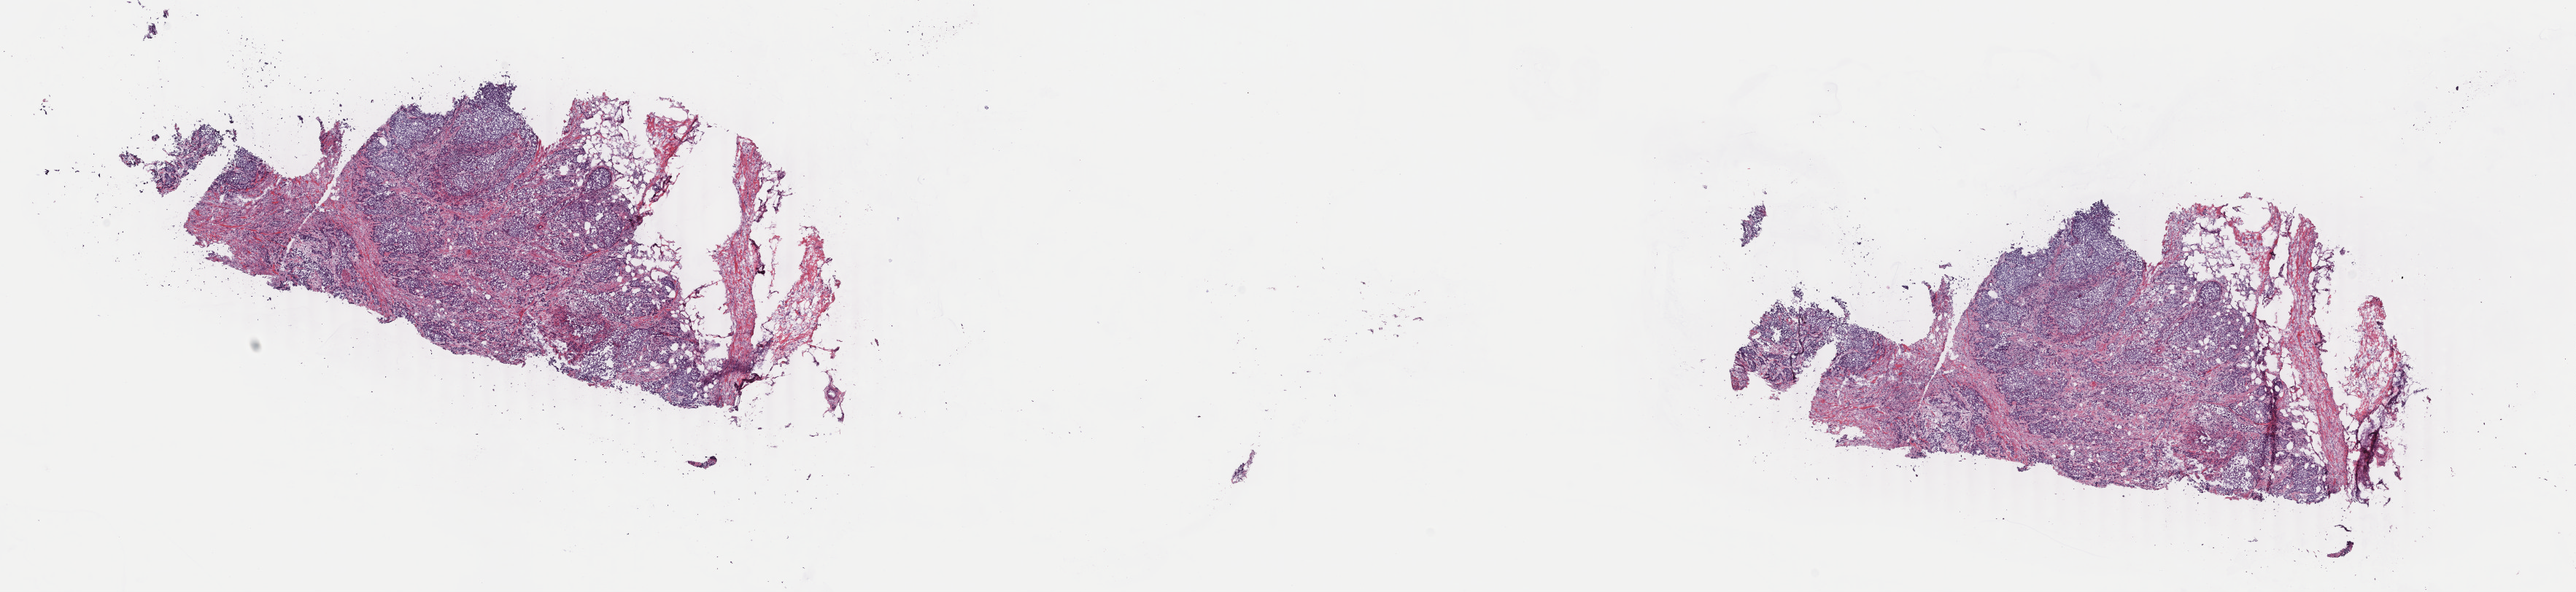
H&E-stained whole-slide image, whole scanned area (about 28.1 x 6.5 mm, slide scanned at 40x) shown as a low-resolution overview; frozen section from the top of the tissue portion; bladder, primary tumour sample. Male patient; age at initial diagnosis 70 years. Histologic grade: high grade. Composition of this section per pathologist review: tumour cells 70%, tumour nuclei 70%, normal cells 0%, stromal cells 30%, necrosis 0%. Inflammatory infiltration, as recorded: lymphocyte infiltration 5%, monocyte infiltration 0%, neutrophil infiltration 0%.
AJCC pathologic stage: IV (6th edition). Lymph nodes positive (case pathology): 1 of 2 examined. Histologic diagnosis: Transitional cell carcinoma (posterior wall of bladder).